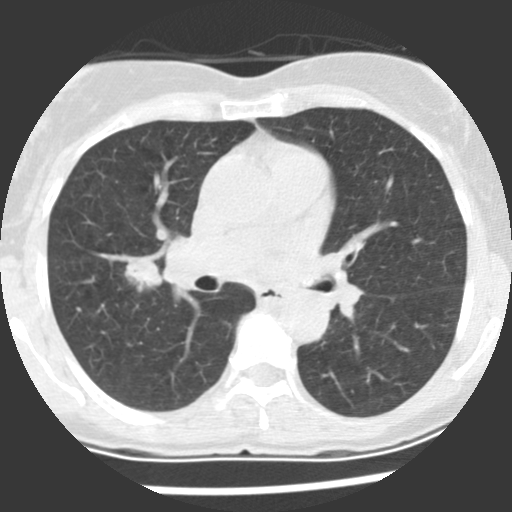
Low-dose screening chest CT, axial slice. Baseline annual screen. Lung window (W 1500 / L -600 HU). 2.5 mm slice thickness. Standard (soft-tissue) reconstruction kernel (STANDARD). 120 kVp. Slice 103 of 225 in the series. Female participant, aged 60 years at enrolment. Current smoker at enrolment.
Expert-annotated lung lesion, box from (x=115, y=253) to (x=173, y=299) px. The screening reader recorded 2 non-calcified nodules or masses ≥4 mm on this exam; which of them this box marks is not recorded. Participant outcome: lung cancer diagnosed 10 days after this screen — adenocarcinoma, NOS, right upper lobe, stage IIIA (AJCC 6th edition), 20 mm at pathology.